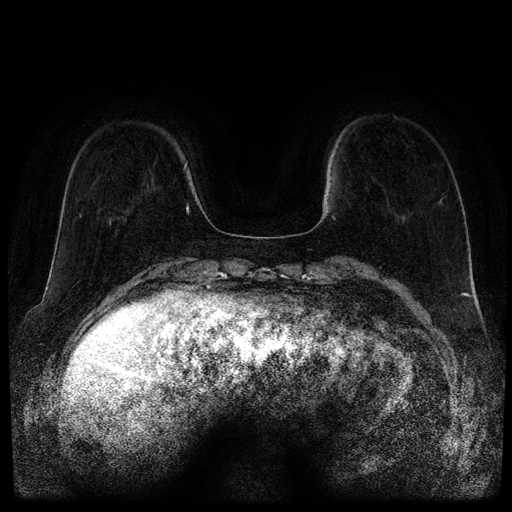
Breast MRI (dynamic contrast-enhanced, multi-phase), one axial slice; position 32 of 116 along the scan axis; dynamic contrast-enhanced series, time point 2 of 5 at this slice position (early post-contrast); 1.5 T; TE 2.6 ms, TR 5.3 ms; 512 × 512 image matrix. Female patient, age 66 years.
Annotated regions visible in this slice (semi-automatic segmentation, software-assisted and operator-edited):
- breast lesion (labelled benign in the annotation): box from (x=109, y=219) to (x=111, y=226) px